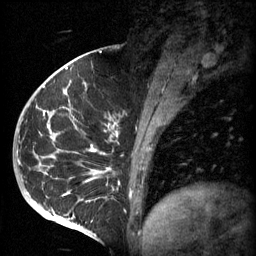
Breast MRI (dynamic contrast-enhanced), one sagittal slice; position 25 of 60 along the scan axis; 3 images stored at this slice position (order not interpretable as contrast timing); 1.5 T; TE 4.2 ms, TR 11 ms; 256 × 256 image matrix, field of view 200 × 200 mm. Female patient, age 51 years.
Outlined on this slice (semi-automatically segmented with operator editing):
- analysis volume of interest (the breast-tissue region the enhancement analysis was run in; not a lesion): box from (x=48, y=82) to (x=161, y=197) px
- tumour enhancement mask (voxels above the 70 % enhancement threshold inside the analysis volume of interest): (x=48, y=82)–(x=152, y=181)